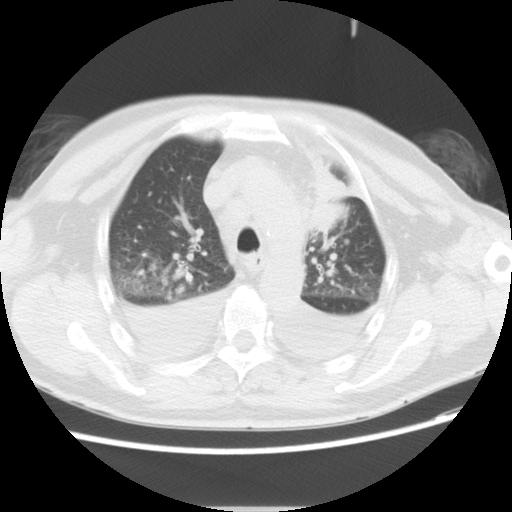
Chest CT, one axial slice. Slice 17 of 19 in the series (ordered by position). Reconstruction kernel STANDARD. Lung window (W 1500 / L -600 HU). 5 mm slice thickness. 512 × 512 image matrix. Patient: male, 66 years. From the clinical record (not read from this slice): clinical TNM (as recorded): T1c N0 M0.
Structures marked on this image (bounding box drawn by a radiologist):
- lung tumour (recorded histology: adenocarcinoma): bounding box <306,145,346,235> (left, top, right, bottom; pixels)